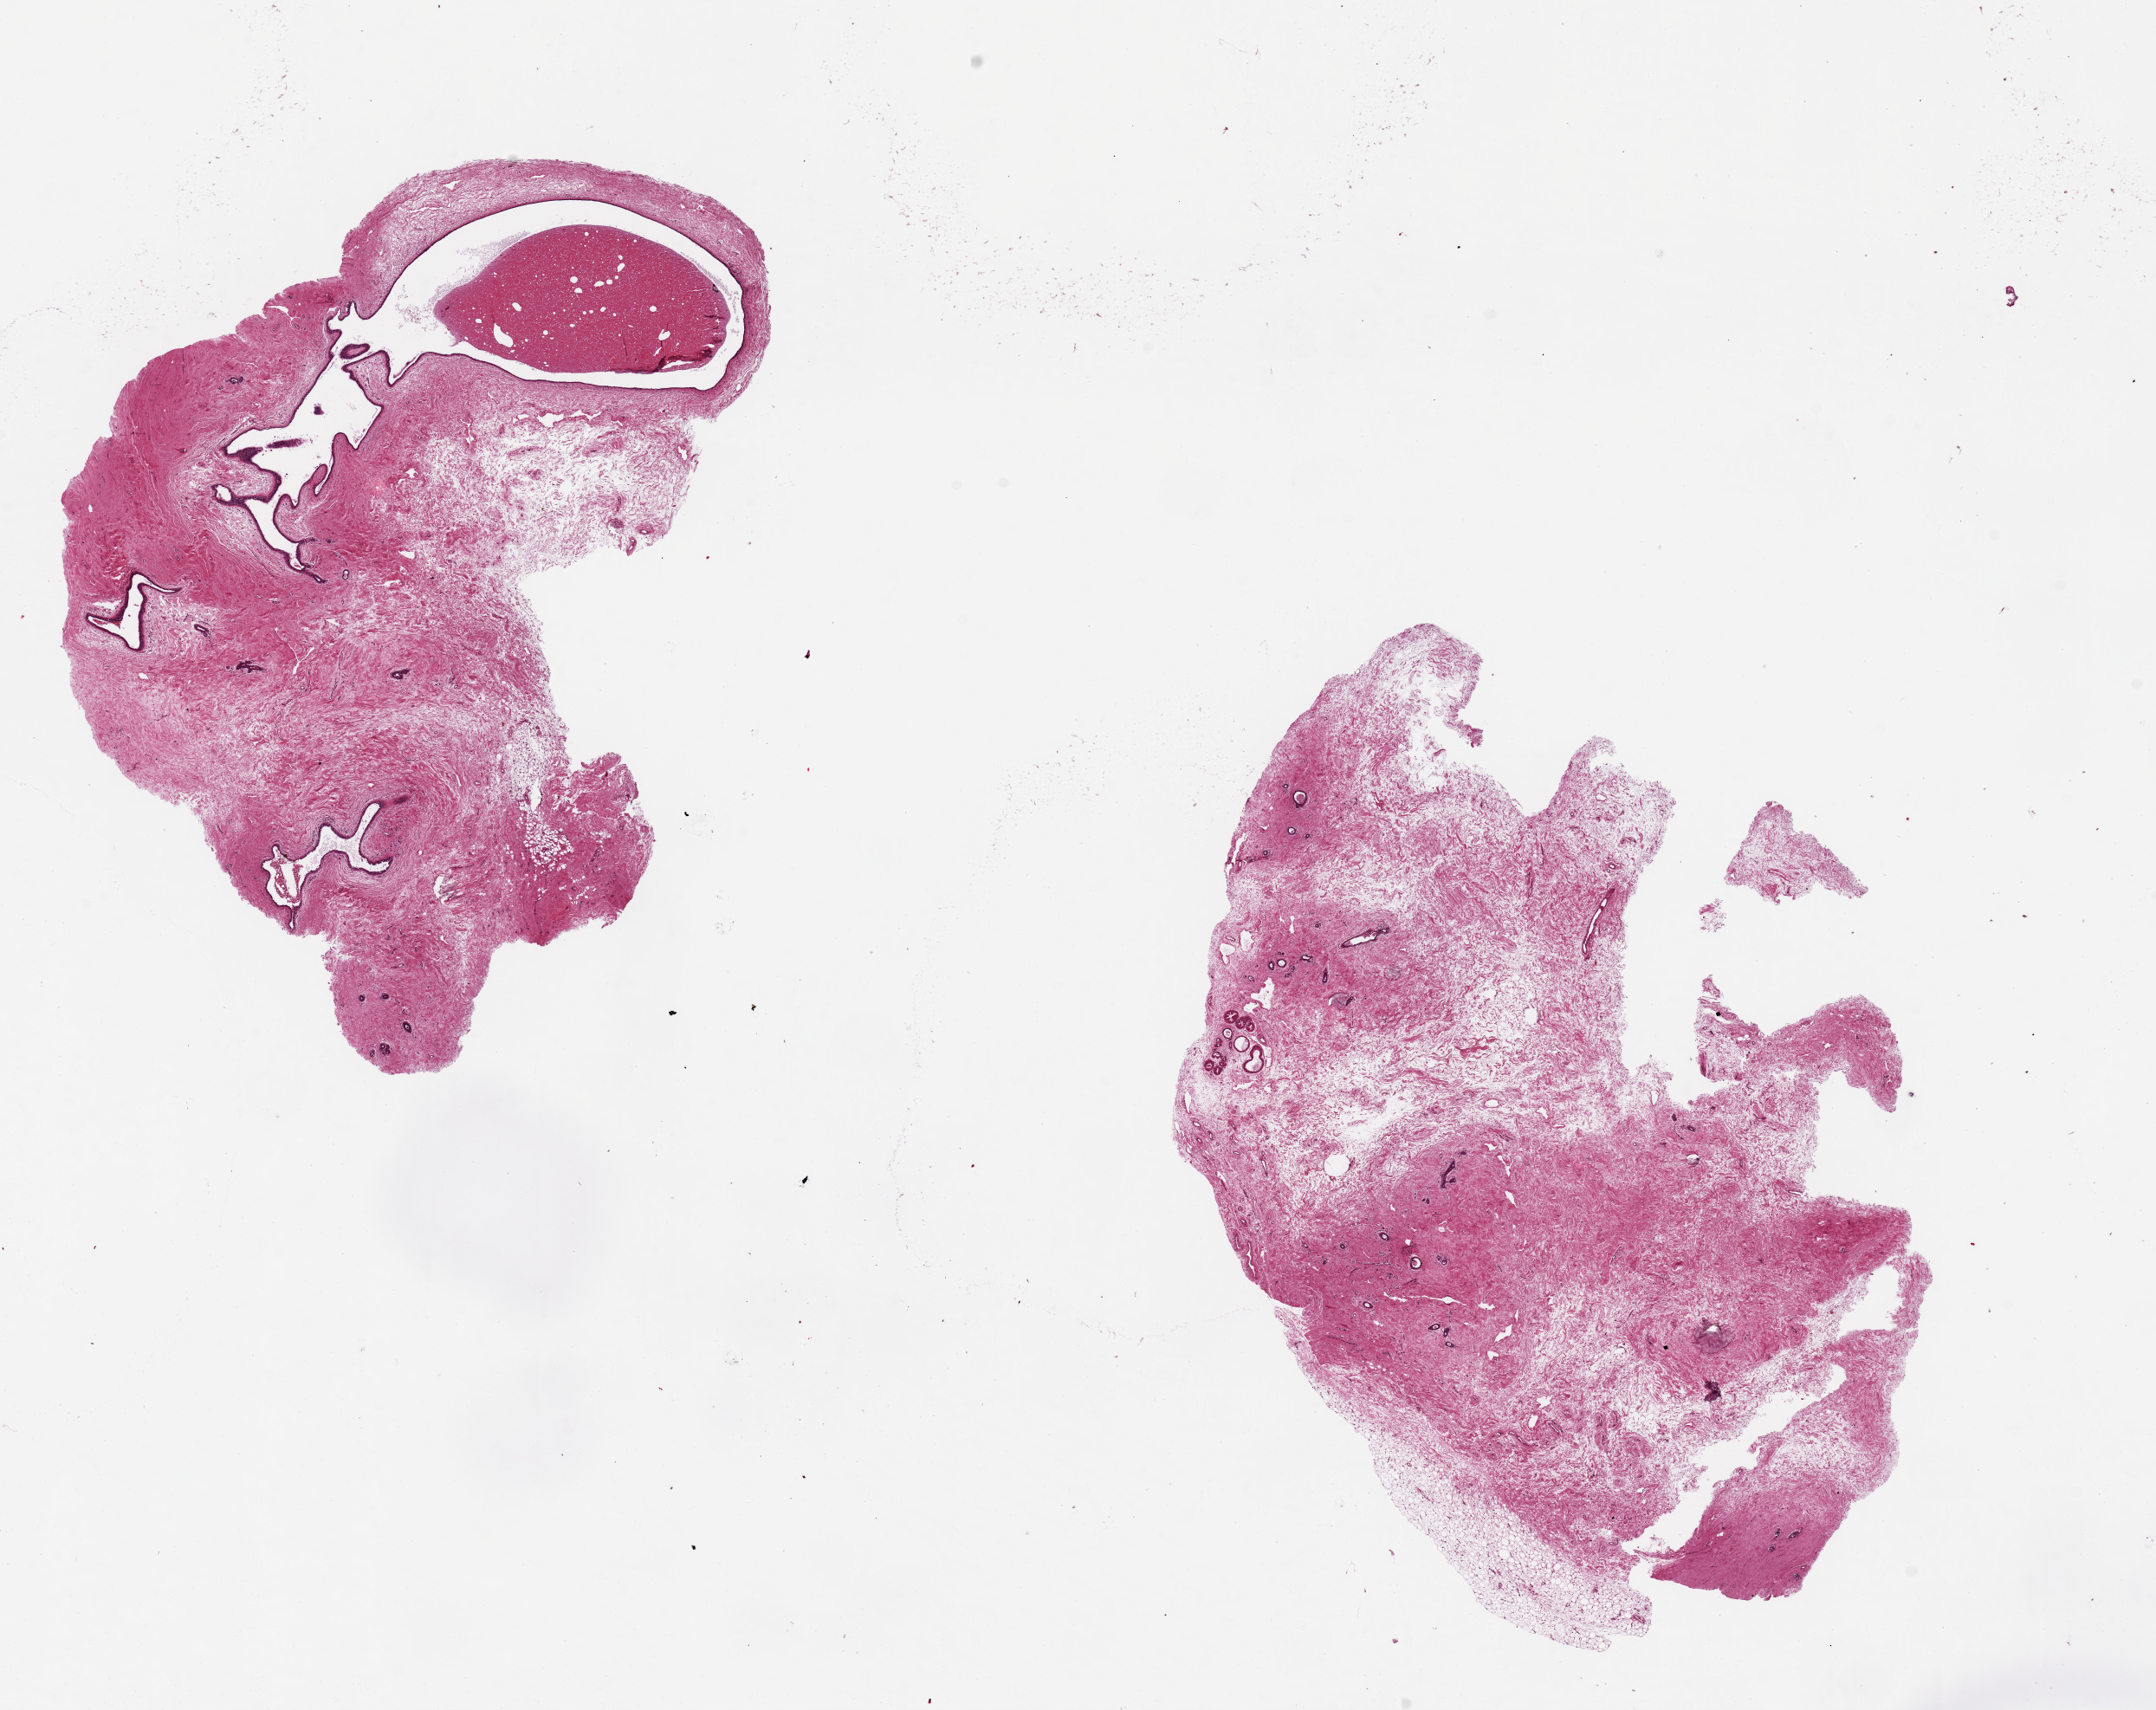
Digitized H&E-stained section, a low-resolution overview of the entire scanned area, about 19.7 x 15.6 mm, PAXgene-fixed paraffin-embedded (PFPE) section, sampled site (target tissue): breast, tissue donor sample. Donor sex: female.
* reviewer comment on this tissue sample: 2 pieces ~8x5mm; Fibrocystic changes; Cystic ducts enircled; normal TDLUs